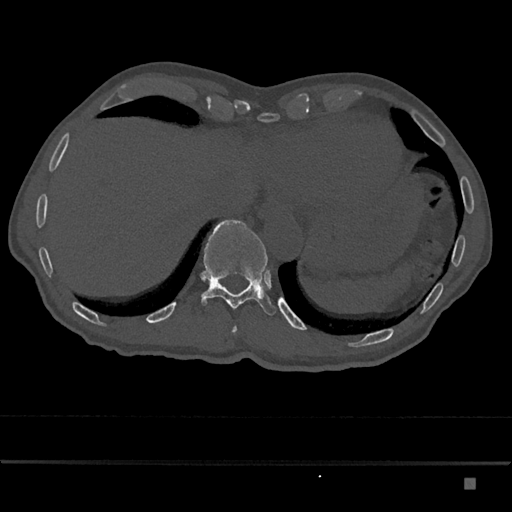
CT including the spine, one axial slice. Position 683 of 797 along the scan axis. 120 kVp. Bone window (W 1800 / L 400 HU). 0.5 mm slice thickness. 512 × 512 image matrix, field of view 390 × 390 mm. Patient: male, 72 years. From the clinical record (not read from this slice): primary cancer: prostate.
Annotated regions visible in this slice (semi-automatically segmented with operator editing):
- T10 vertebra: box from (x=233, y=327) to (x=237, y=333) px
- T11 vertebra: (x=201, y=219)–(x=276, y=315)